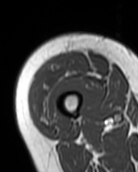
MRI of an extremity soft-tissue mass, one axial slice. Position 22 of 99 along the scan axis. MR volume resampled by the dataset authors to the PET/CT grid (not the native acquisition matrix). 3.27 mm slice thickness. 138 × 172 image matrix. Female patient. Case-level facts recorded for this patient, not image findings: histological type: pleiomorphic undifferentiated sarcoma; grade: high; site of the primary tumour: right quadricep.
Outlined on this slice (expert contour drawn on MRI and transferred to this co-registered scan by the dataset authors):
- gross tumour volume including surrounding oedema: box from (x=32, y=52) to (x=88, y=122) px